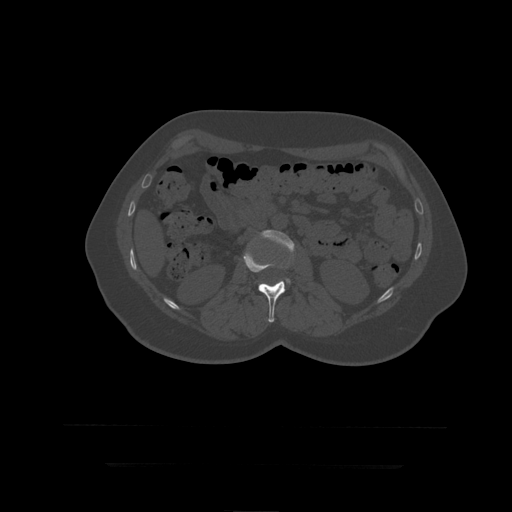
CT including the spine, one axial slice. Position 141 of 399 along the scan axis. Reconstruction kernel STANDARD. 120 kVp. Bone window (W 1800 / L 400 HU). 512 × 512 image matrix. Patient age 41 years. From the clinical record (not read from this slice): primary cancer: breast.
Outlined on this slice (semi-automatically segmented with operator editing):
- L2 vertebra: bounding box <244,249,286,323> (left, top, right, bottom; pixels)
- L3 vertebra: <261,230,295,283>